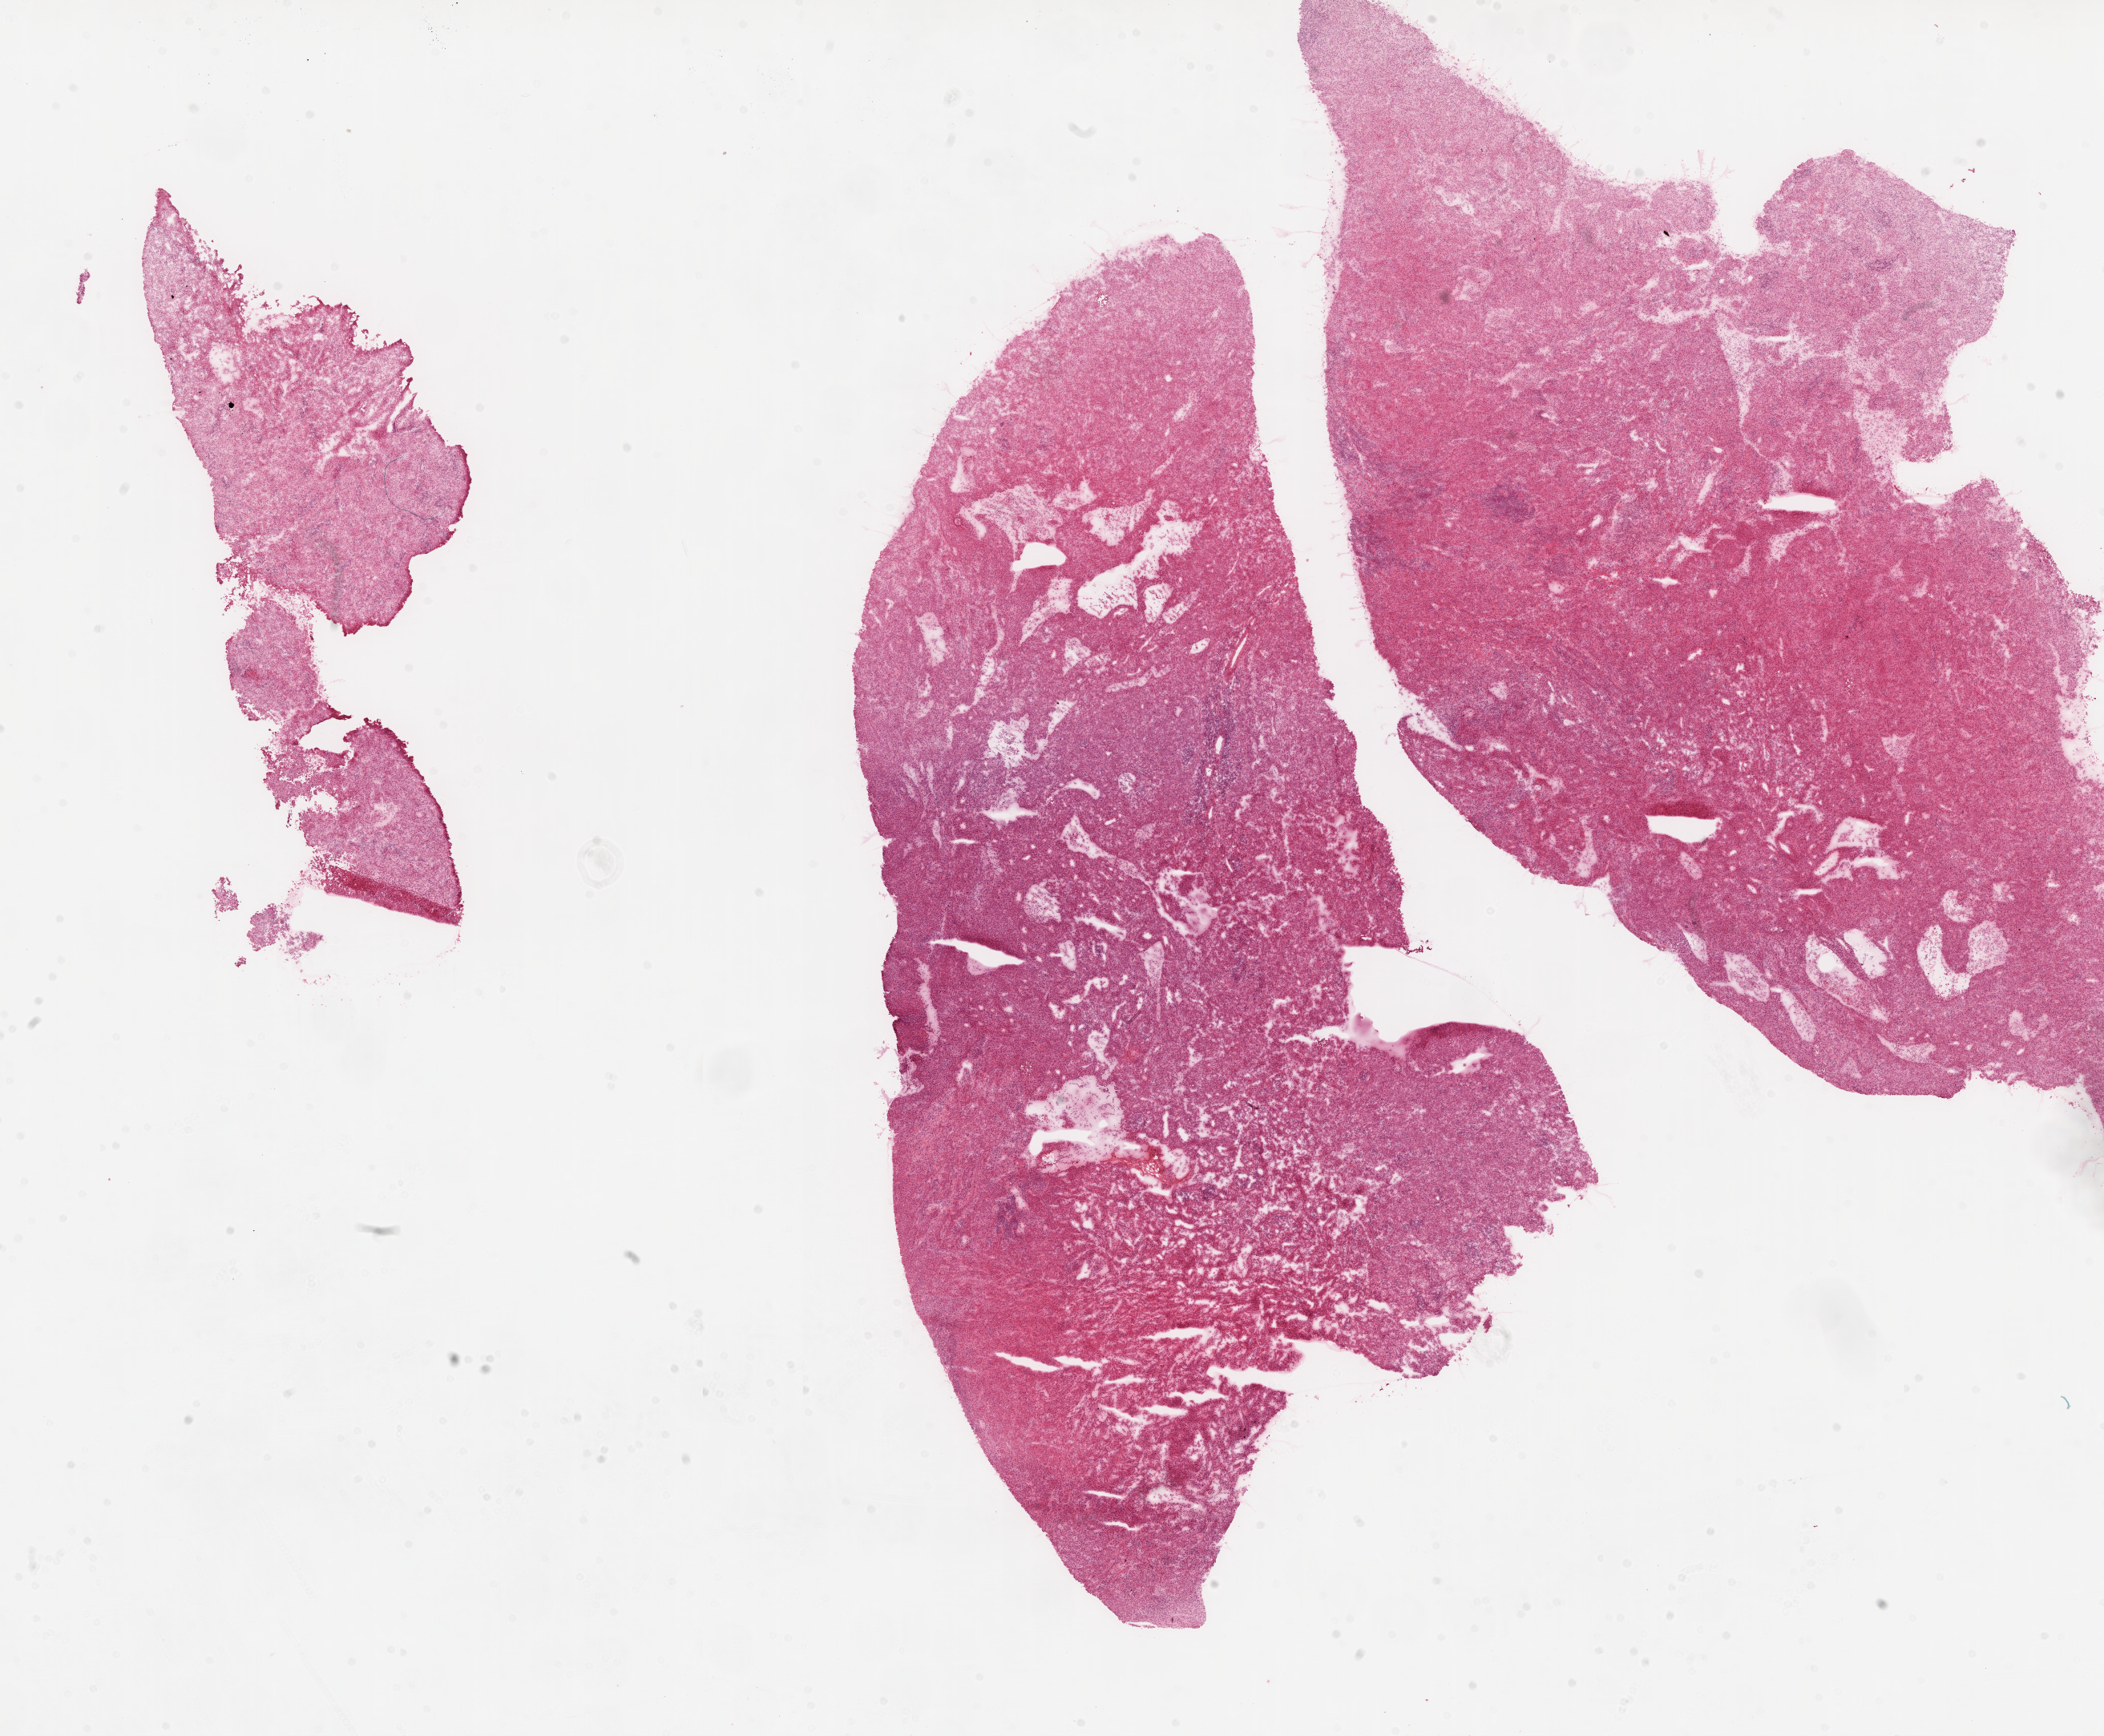
Whole-slide histology image, Hematoxylin and eosin (H&E) stained, low-resolution overview of the scanned area, about 21.1 x 17.4 mm (from a 20x scan); frozen section from the top of the tissue portion; sample: primary tumour, lung. Patient: male, age at initial diagnosis 40 years. Slide review estimates, as recorded: tumour cells 95%, tumour nuclei 80%, normal cells 0%, stromal cells 5%, necrosis 0%.
• pathologic diagnosis: Squamous cell carcinoma, NOS (upper lobe, lung)
• AJCC pathologic stage: IB (4th edition)